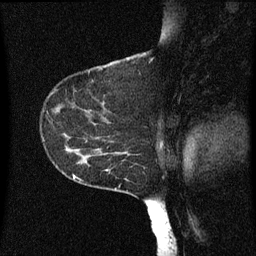
Breast MRI (dynamic contrast-enhanced), one sagittal slice. Position 42 of 60 along the scan axis. Dynamic contrast-enhanced series, image 2 of 3 at this slice position (ordered by acquisition). 1.5 T. TE 4.2 ms, TR 8 ms. 256 × 256 image matrix, field of view 200 × 200 mm. Patient: female, 55 years.
Outlined on this slice (semi-automatic segmentation, software-assisted and operator-edited):
- analysis volume of interest (the breast-tissue region the enhancement analysis was run in; not a lesion): box from (x=46, y=124) to (x=151, y=183) px
- tumour enhancement mask (voxels above the 70 % enhancement threshold inside the analysis volume of interest): (x=96, y=138)–(x=127, y=155)